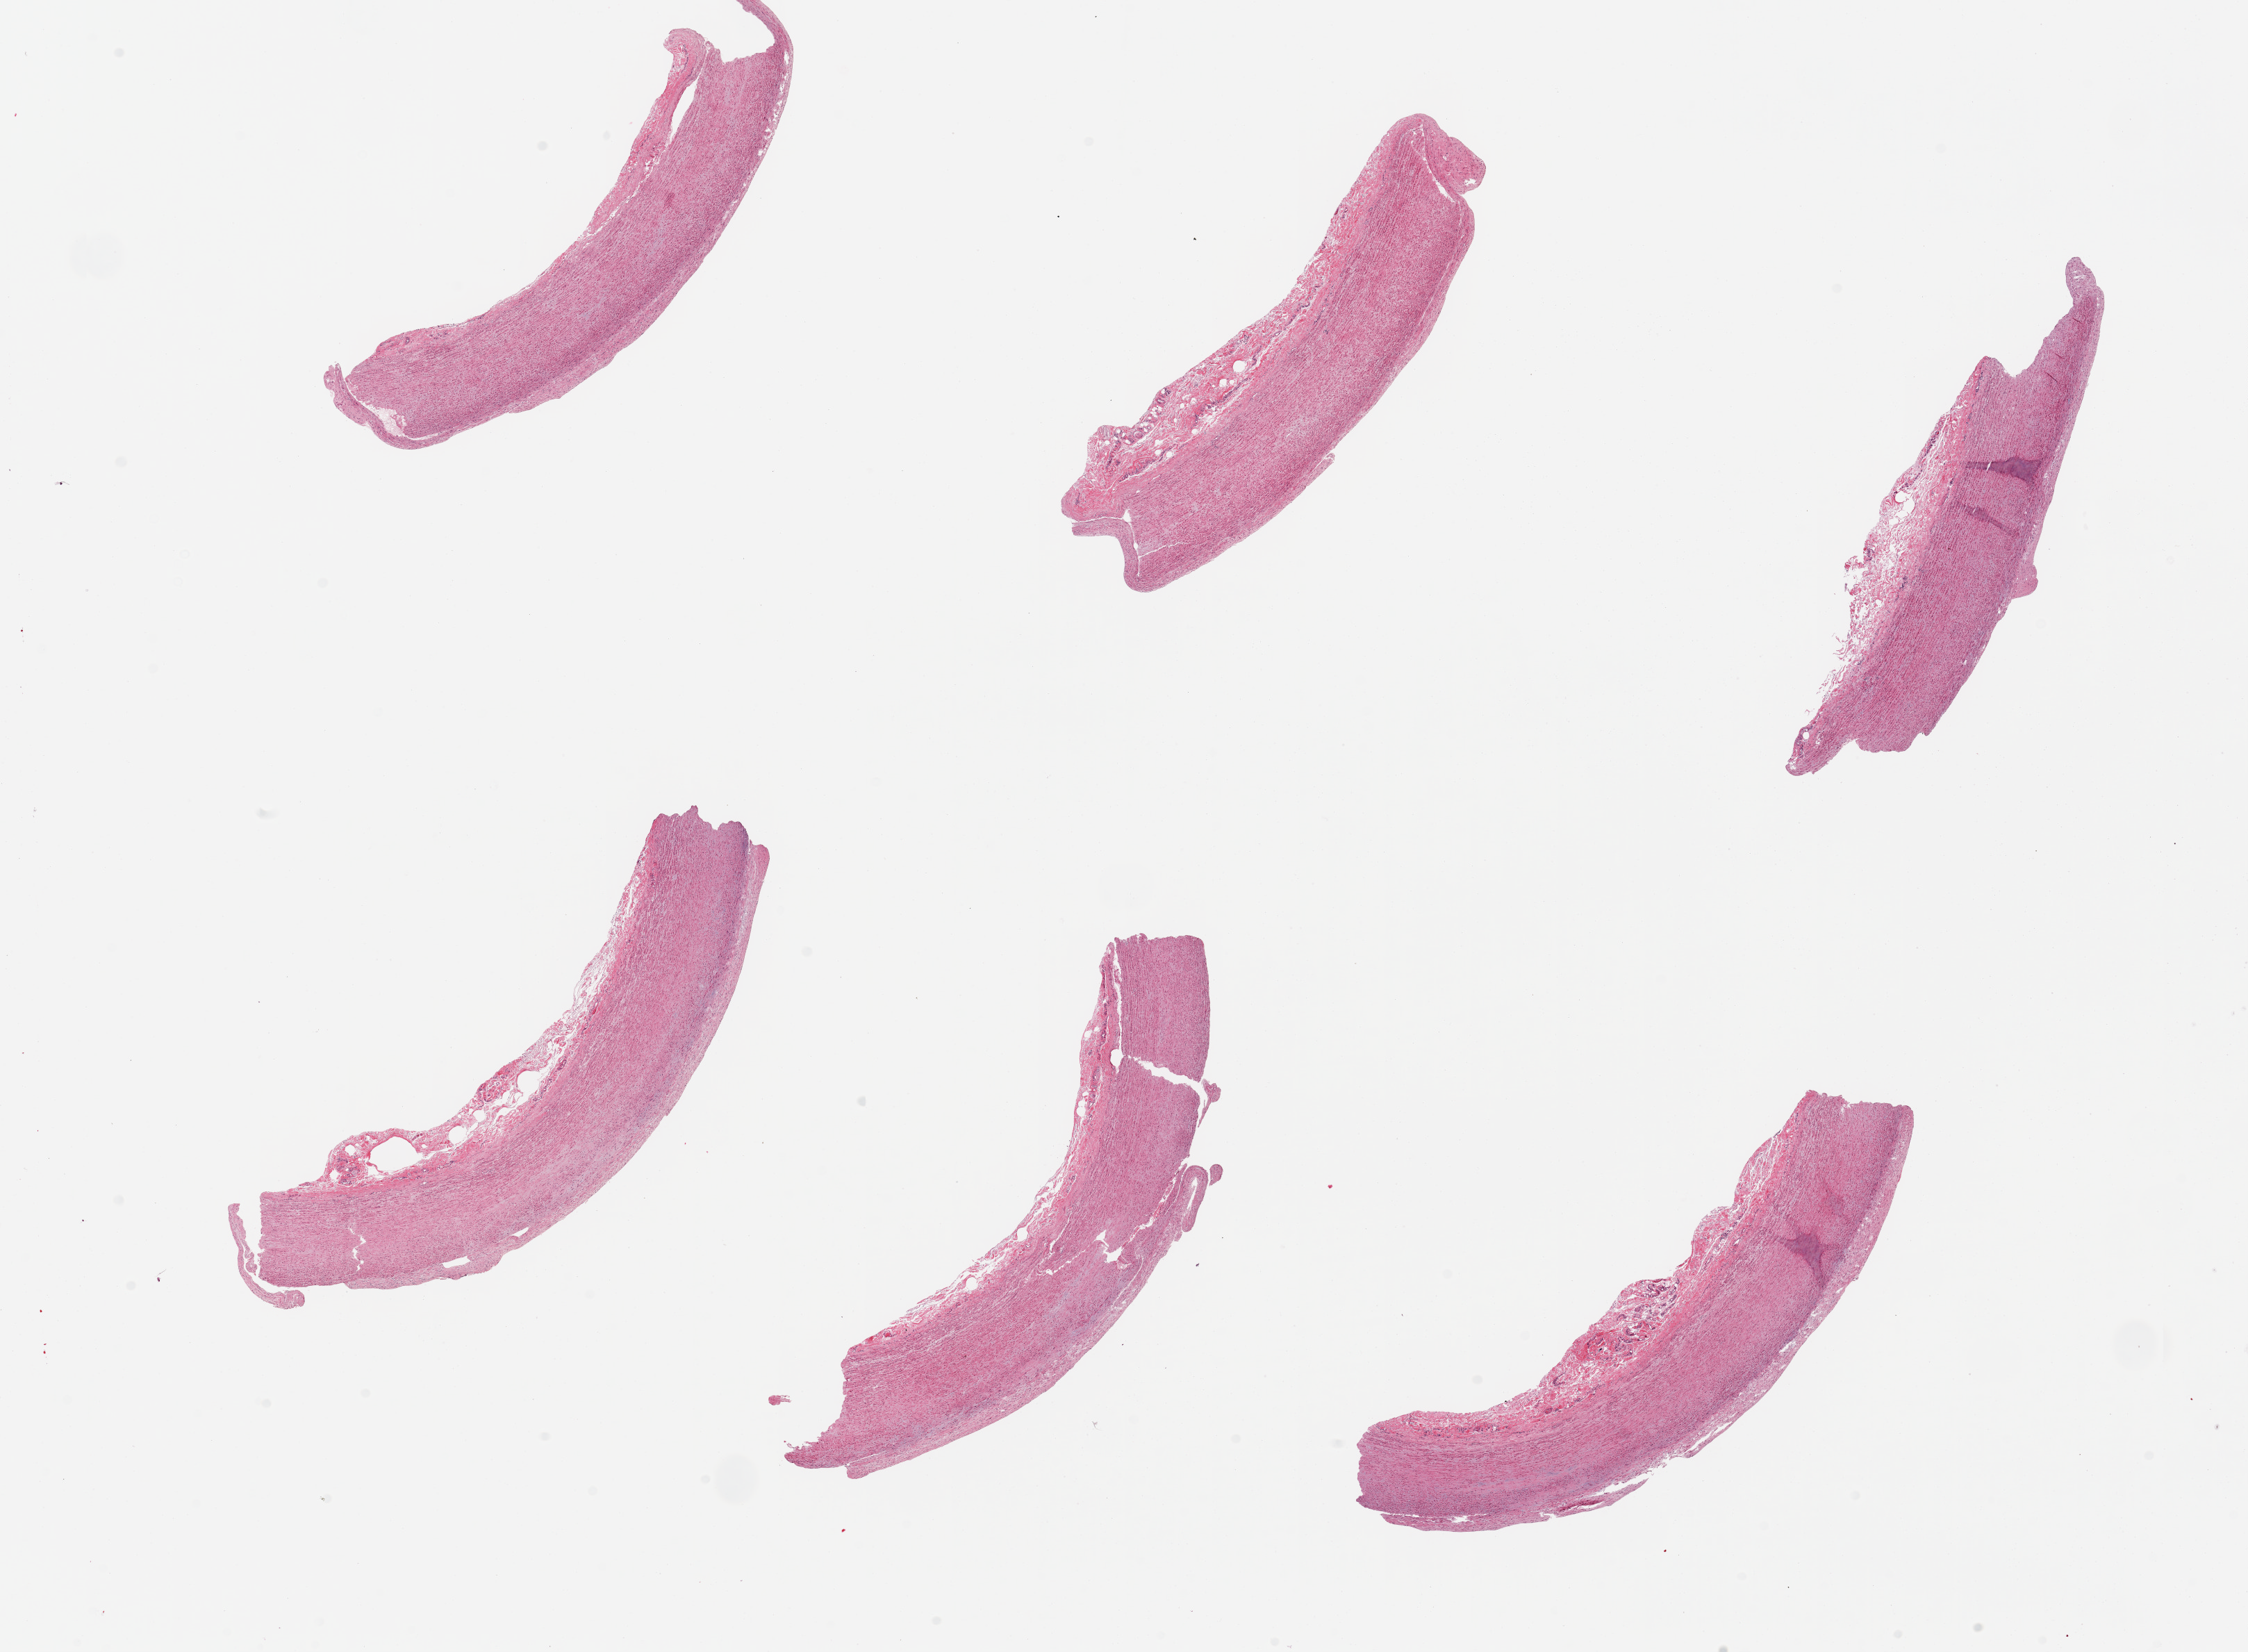
Digitized hematoxylin and eosin (H&E)-stained section, a low-resolution overview of the entire scanned area, about 25.6 x 18.8 mm, PAXgene-fixed paraffin-embedded (PFPE) section, sampled site (target tissue): aorta, tissue donor sample. Donor sex: male.
Reviewer comment on this tissue sample: 6 pieces, minimla atherosis.